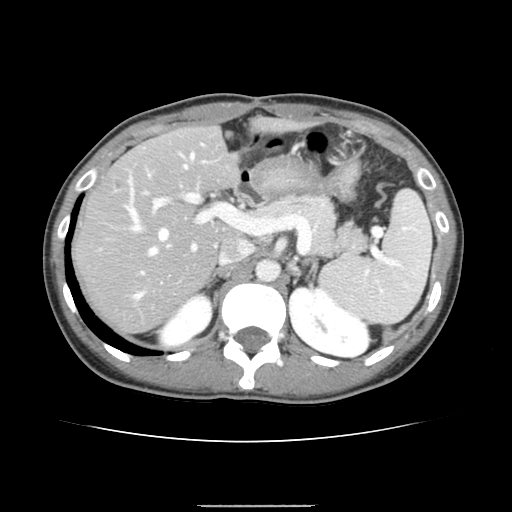
Contrast-enhanced abdominal CT, one axial slice; position 95 of 150 along the scan axis; intravenous contrast given; soft-tissue window (W 400 / L 40 HU); 2.5 mm slice thickness; 512 × 512 image matrix. Female patient, age 32 years. From the clinical record (not read from this slice): diagnosis: colorectal cancer liver metastases, imaged before liver resection; multiple liver metastases: yes; largest metastasis: 0.7 cm; chemotherapy before resection: yes.
Structures marked on this image (outlined manually by an expert reader):
- hepatic veins: bounding box <127,153,194,298> (left, top, right, bottom; pixels)
- liver: <76,127,239,333>
- planned liver remnant (the part of the liver to remain after resection): <76,127,239,280>
- portal vein (with intrahepatic branches): <126,161,234,273>
- liver metastasis: <114,181,121,188>